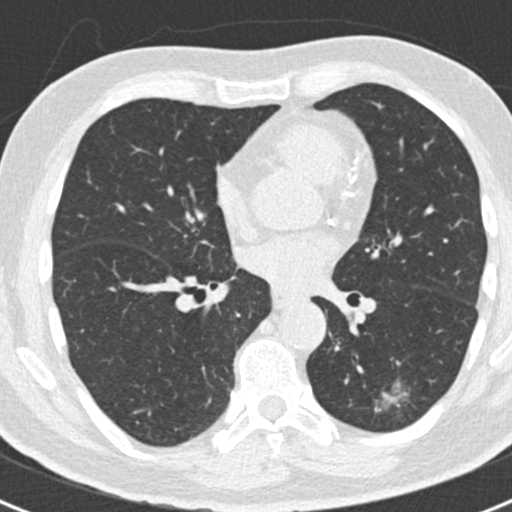
Low-dose screening chest CT, axial slice, first (baseline) screen, lung window (W 1500 / L -600 HU), 2 mm slice thickness, 120 kVp. Male participant, aged 66 years at enrolment. Former smoker at enrolment.
Expert reader's lesion annotation, box from (x=348, y=344) to (x=421, y=423) px. Screening reader's record for this exam (one nodule recorded; not confirmed to be the boxed lesion): non-calcified nodule or mass ≥4 mm, left lower lobe, 43 × 27 mm, smooth margins. Later outcome: lung cancer diagnosed 801 days after this screen — adenocarcinoma, NOS, left lower lobe, poorly differentiated (G3), stage IB (AJCC 6th edition), 38 mm at pathology.